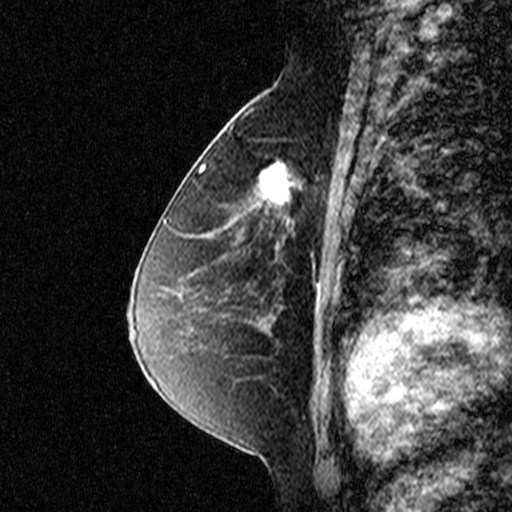
Breast MRI (dynamic contrast-enhanced), one sagittal slice; position 24 of 44 along the scan axis; dynamic contrast-enhanced study with each time point stored as its own series, time point 2 of 3 at this slice position (early post-contrast, ordered by acquisition time); 1.5 T; TE 4.5 ms, TR 11 ms; 3 mm slice thickness; 512 × 512 image matrix. Patient: female, 49 years. Case-level facts recorded for this patient, not image findings: setting: breast cancer imaged before/during neoadjuvant chemotherapy; receptor status: triple-negative.
Outlined on this slice (semi-automatic segmentation, software-assisted and operator-edited):
- analysis volume of interest (the breast-tissue region the enhancement analysis was run in; not a lesion): bounding box (x1, y1, x2, y2) in pixels: (238, 122, 331, 227)
- tumour enhancement mask (voxels above the 90 % enhancement threshold inside the analysis volume of interest): (261, 158, 307, 226)